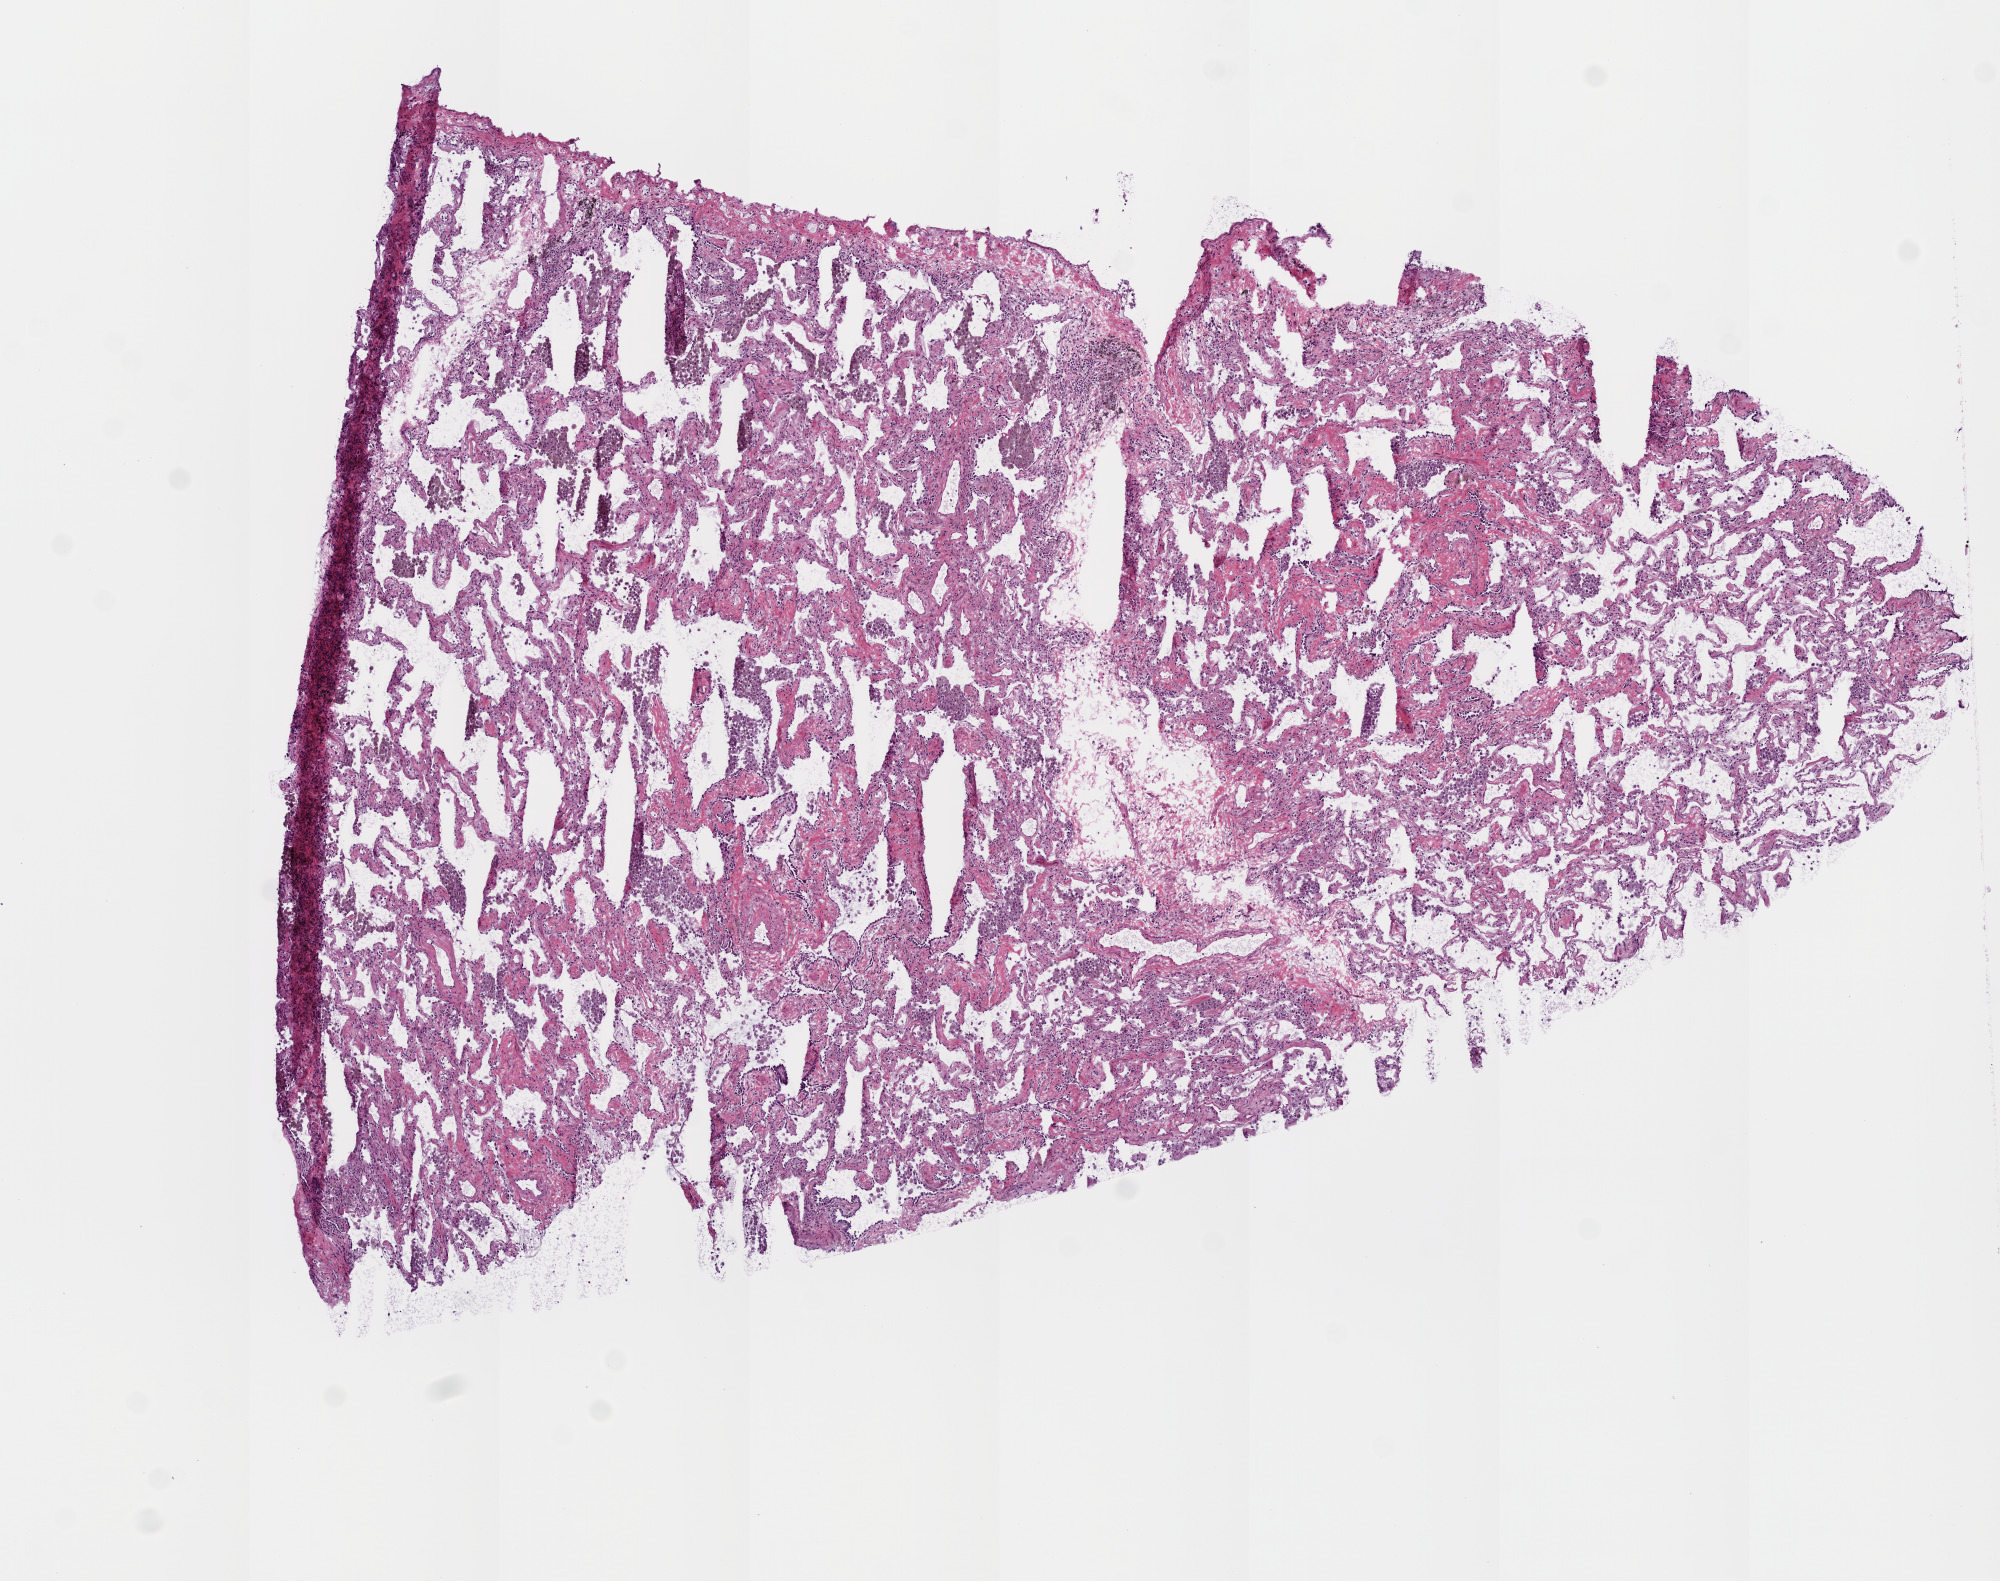
Whole-slide histology image, H&E — whole scanned area (about 8.0 x 6.3 mm, slide scanned at 20x) shown as a low-resolution overview, frozen section, solid tissue normal (non-tumour tissue) sample from the lung. Male, age 51 years at initial diagnosis.
This section: solid tissue normal (non-tumour) sample from the same patient. Patient diagnosis: Adenocarcinoma, NOS.